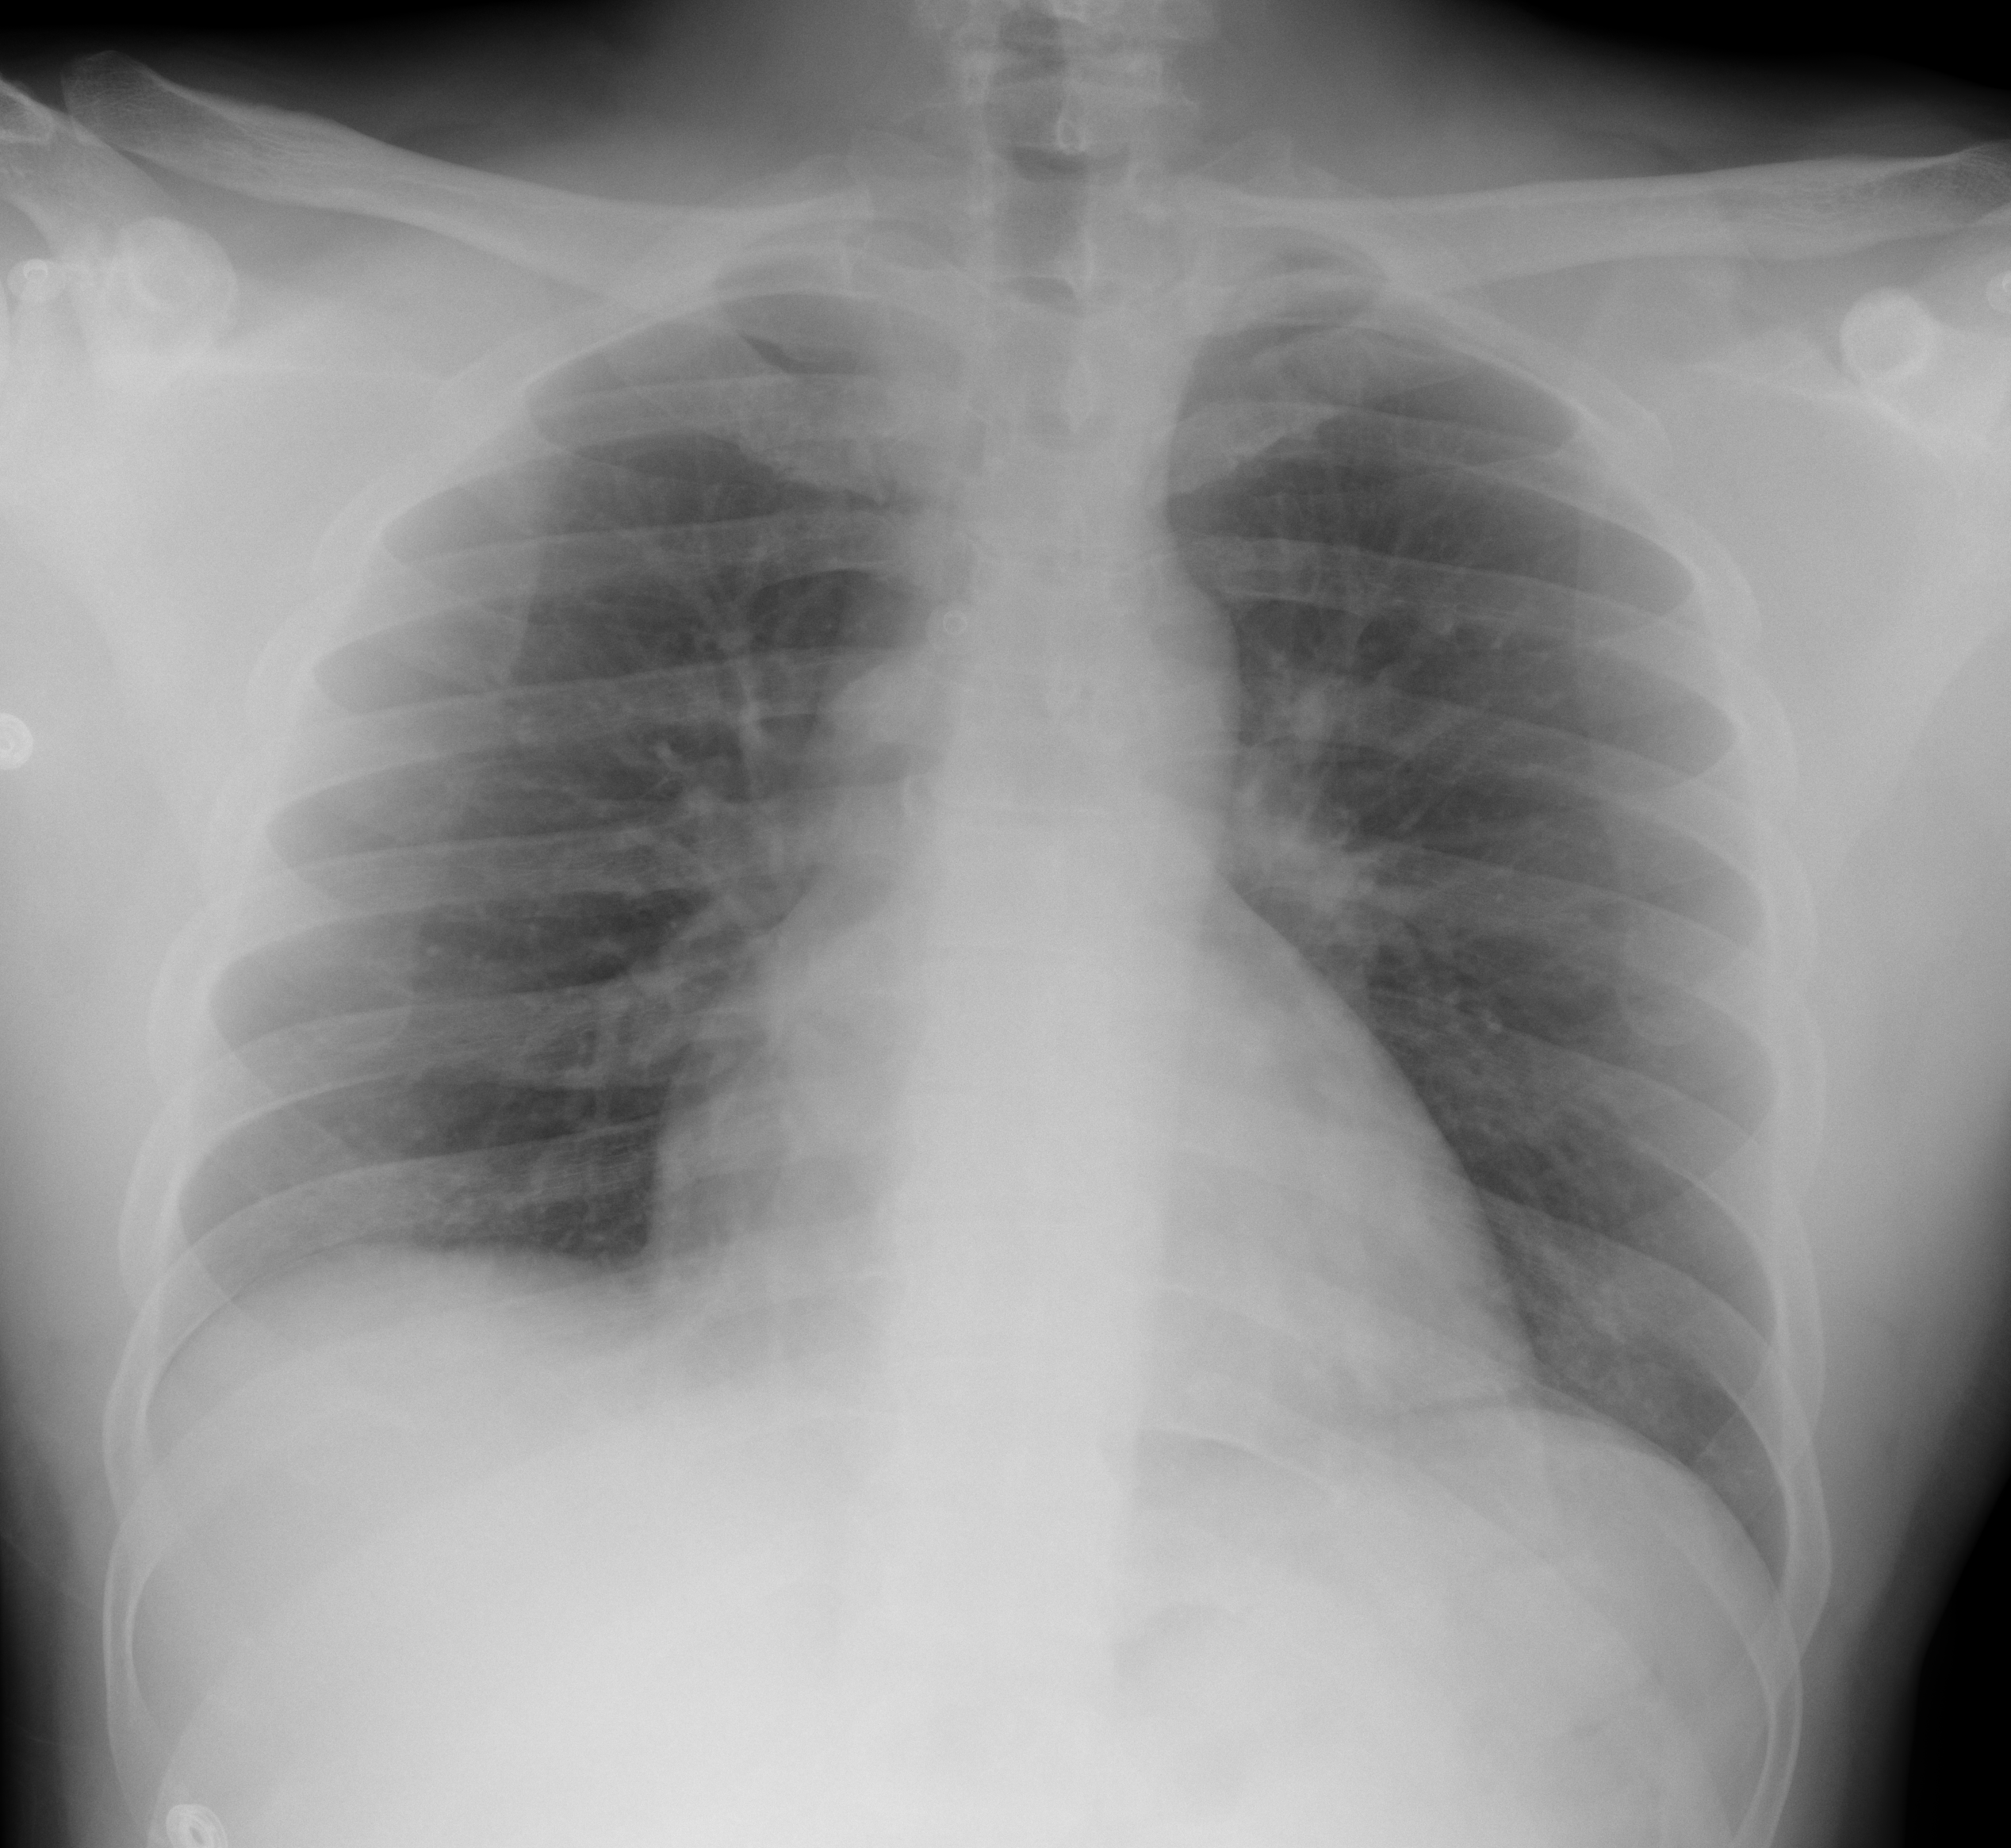
Chest X-ray (portable), AP projection. Male patient, age 44 years; imaged 3 days after the COVID-19 diagnosis.
Radiologist key findings (as recorded): no evidence of any pneumonic infiltration or pleural effusion.